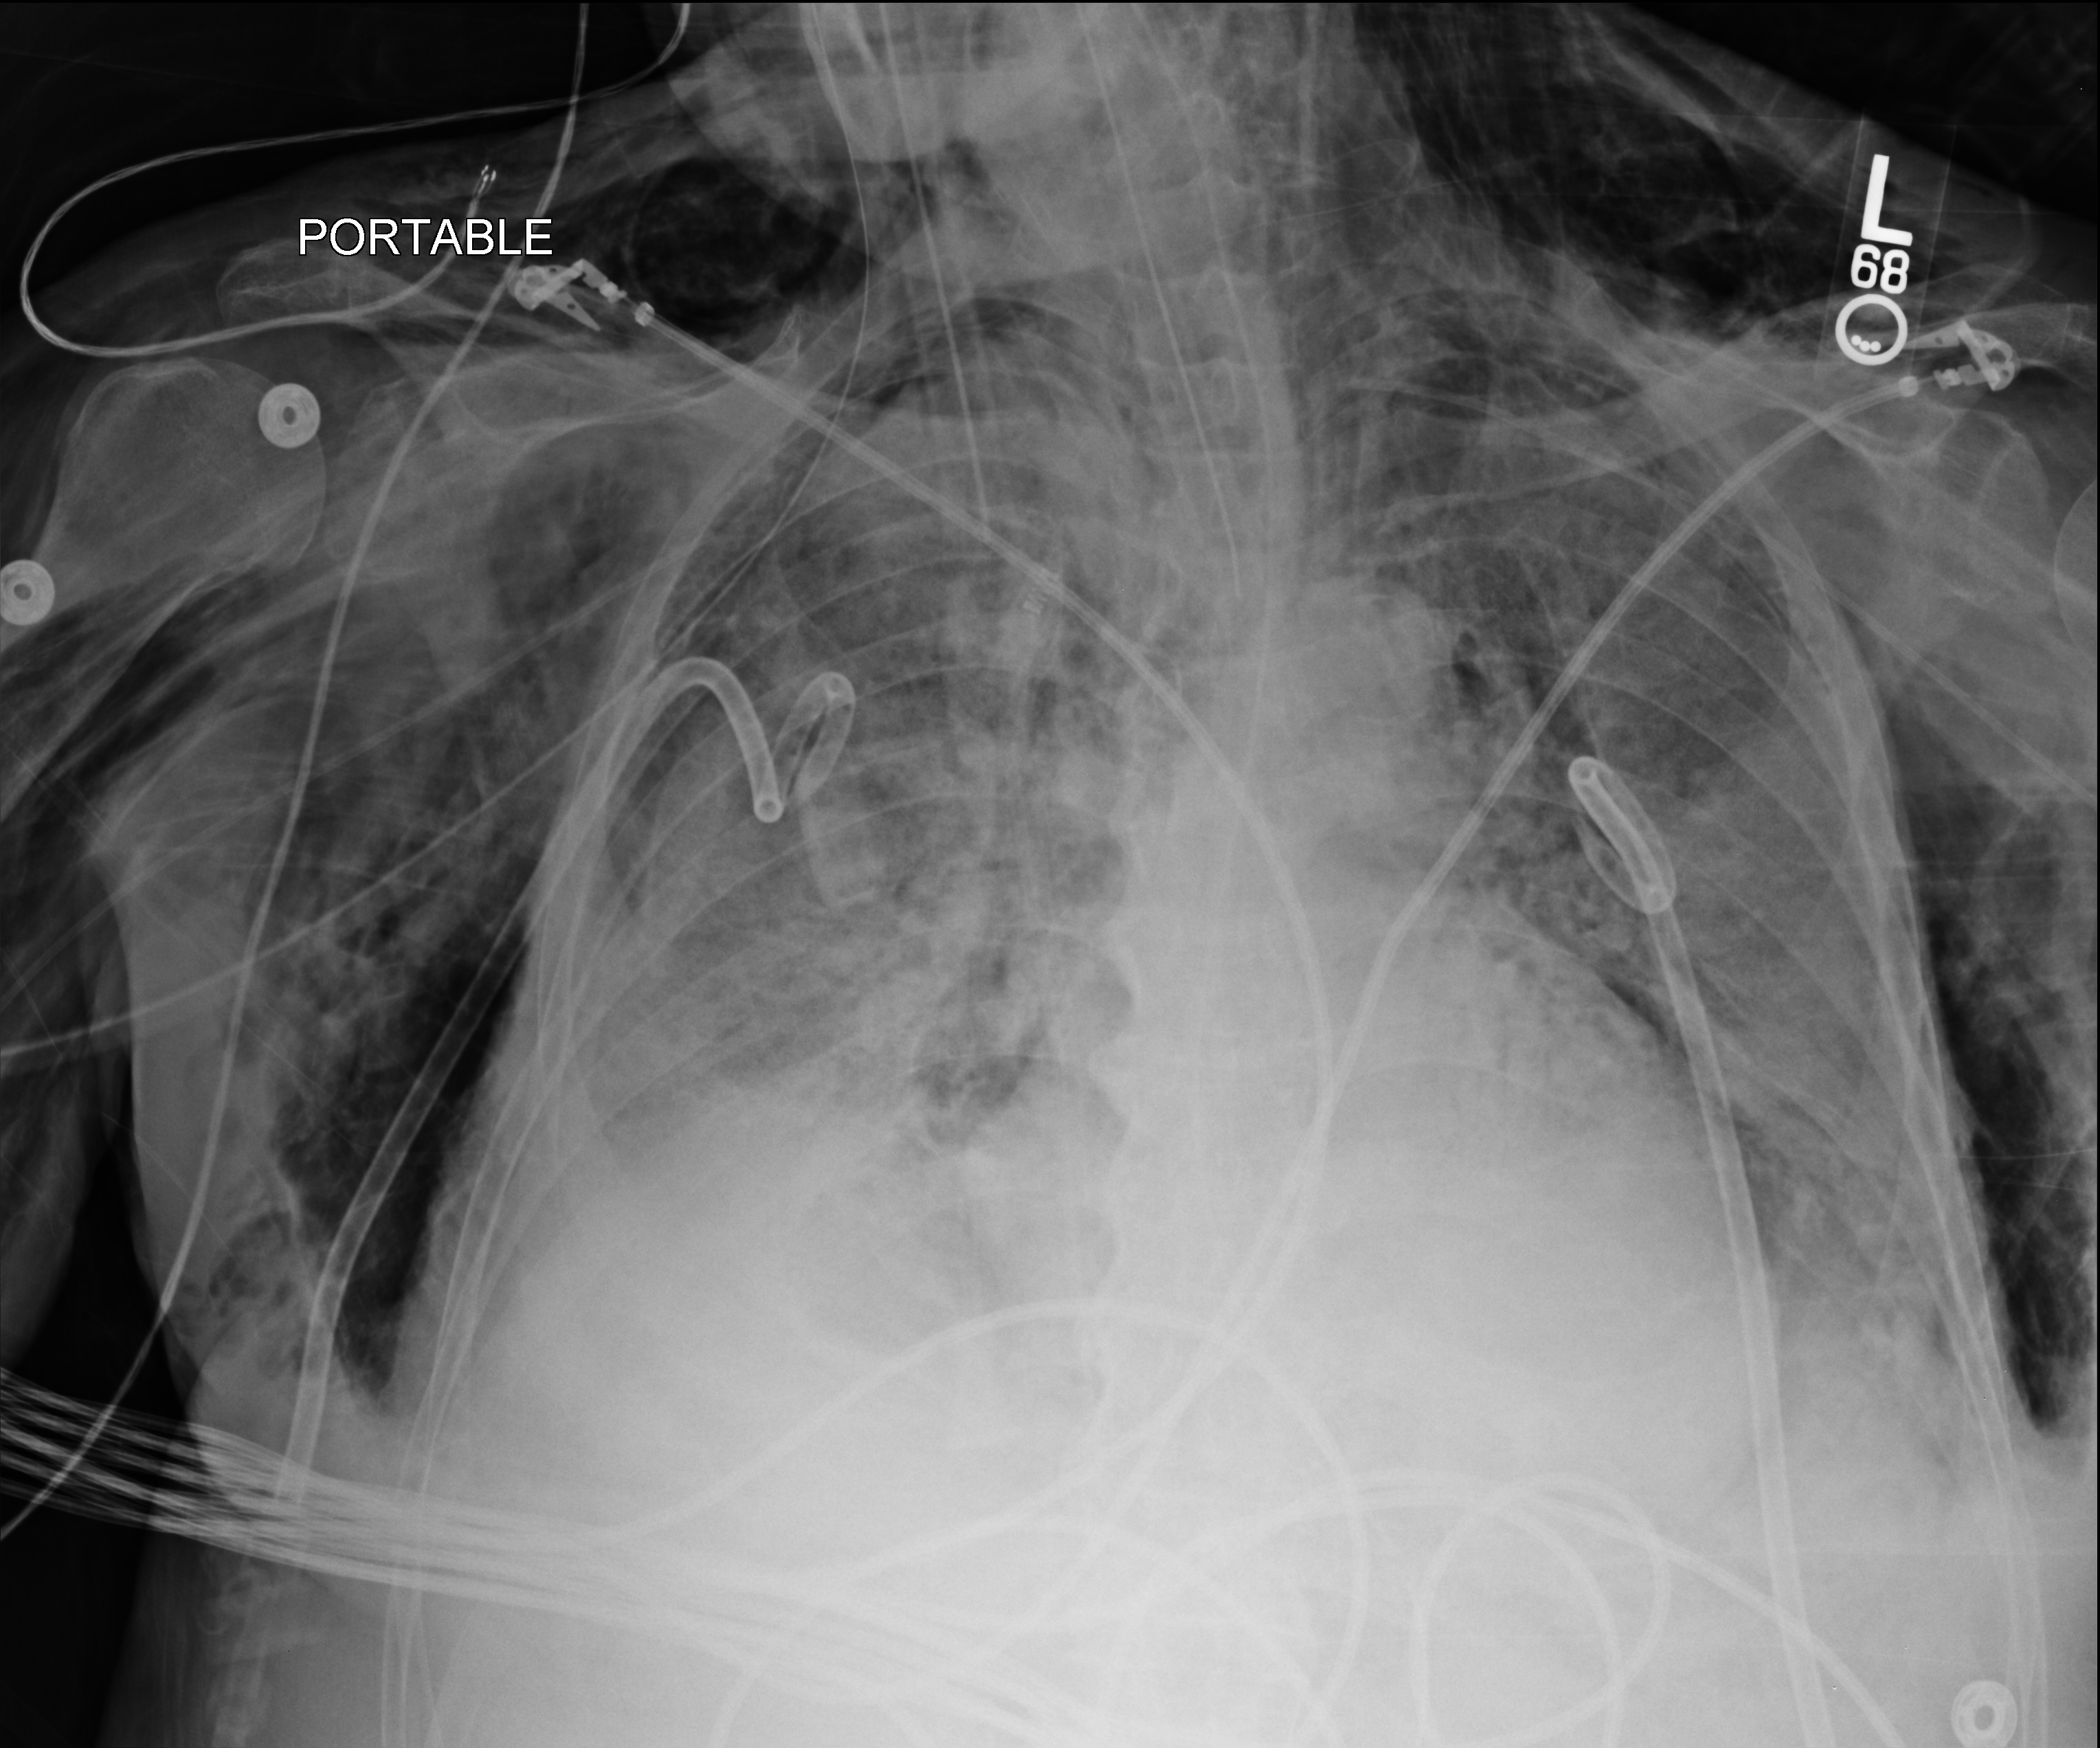
Portable chest radiograph; anteroposterior (AP) projection. Patient hospitalised with COVID-19; male, aged 75–90 years.
Hospital-stay facts (about this admission, not read from this image; timing relative to this image not recorded):
- chronic kidney disease (admission record): no